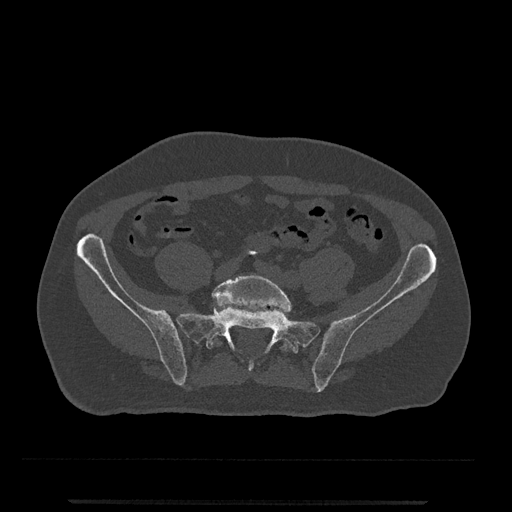
CT including the spine, one axial slice; 120 kVp; bone window (W 1800 / L 400 HU); 0.5 mm slice thickness; 512 × 512 image matrix, field of view 419 × 419 mm. Male patient, age 63 years. From the clinical record (not read from this slice): primary cancer: prostate.
Structures marked on this image (semi-automatic segmentation, software-assisted and operator-edited):
- L5 vertebra: bounding box [x1, y1, x2, y2] px = [209, 274, 292, 352]